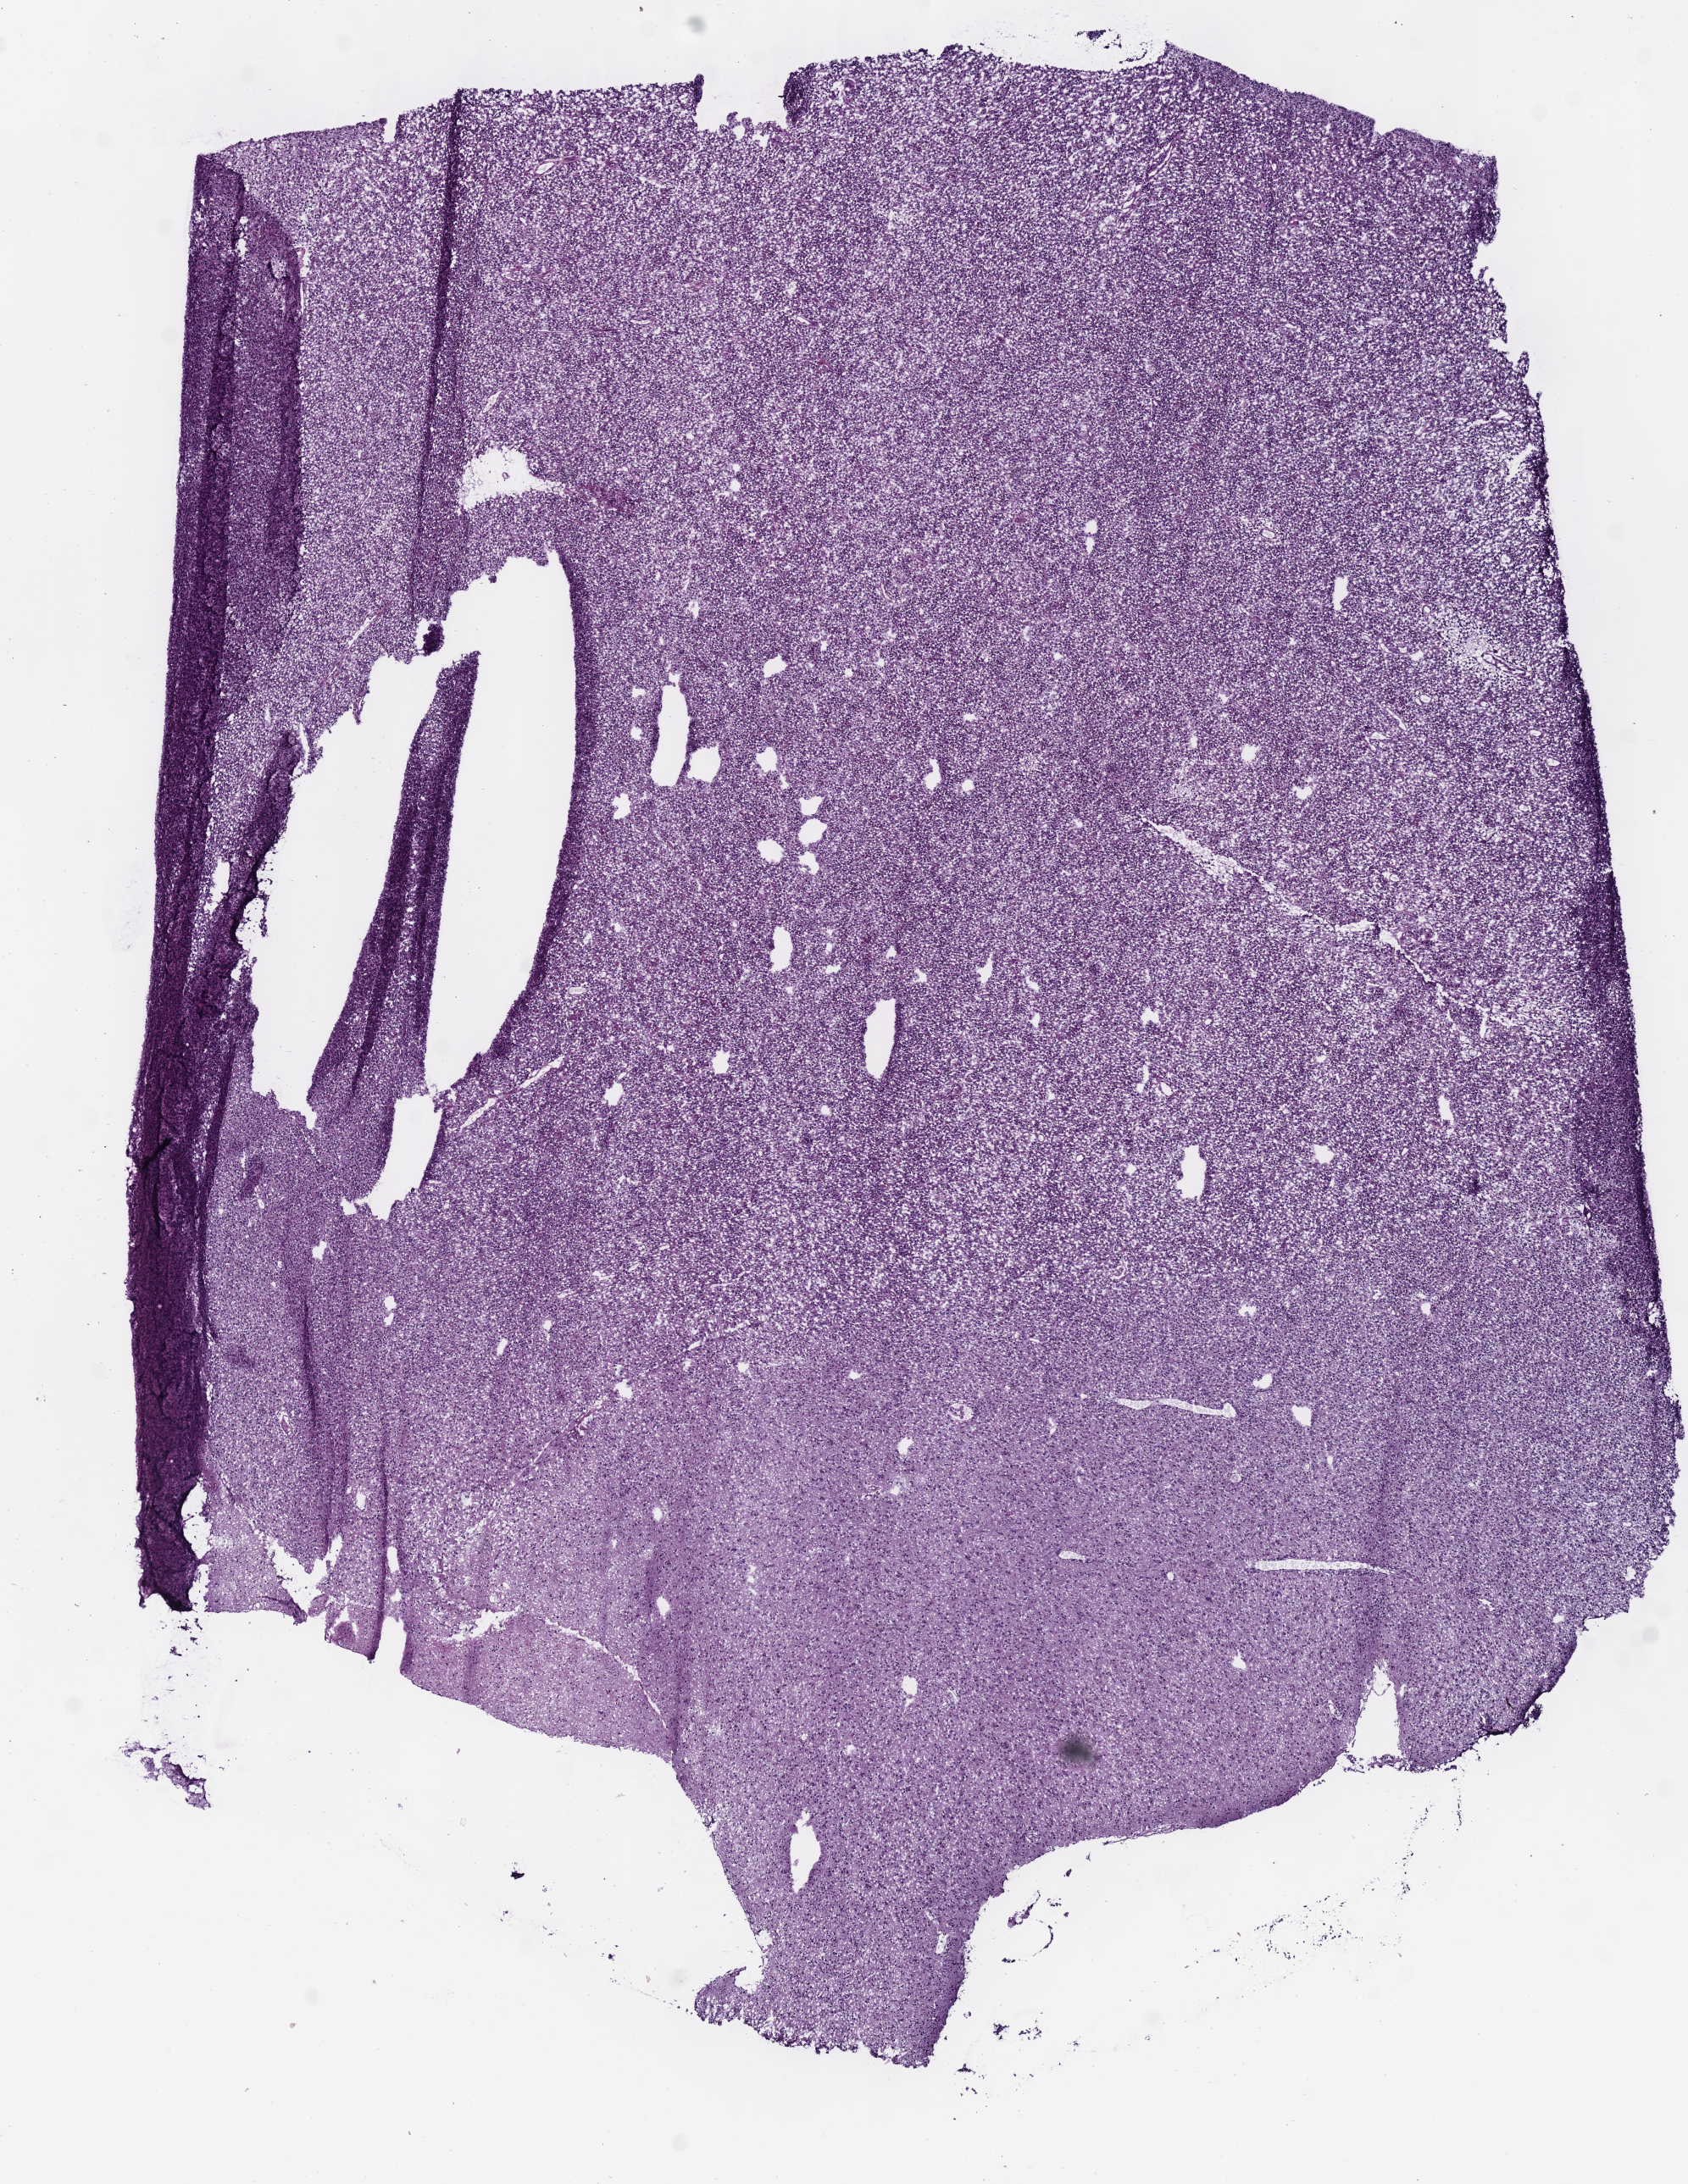
Digitized Hematoxylin and eosin (H&E) stained tissue section (whole slide), low-resolution overview of the scanned area, about 7.8 x 10.1 mm (slide scanned at 40x). Frozen section. Sample: primary tumour, brain. Male patient; age at initial diagnosis 55 years. Histologic grade: G3 (poorly differentiated). Slide review estimates, as recorded: tumour cells 100%, tumour nuclei 80%, normal cells 0%, stromal cells 0%, necrosis 0%.
Histologic diagnosis: Astrocytoma, anaplastic (cerebrum). Laterality: right.